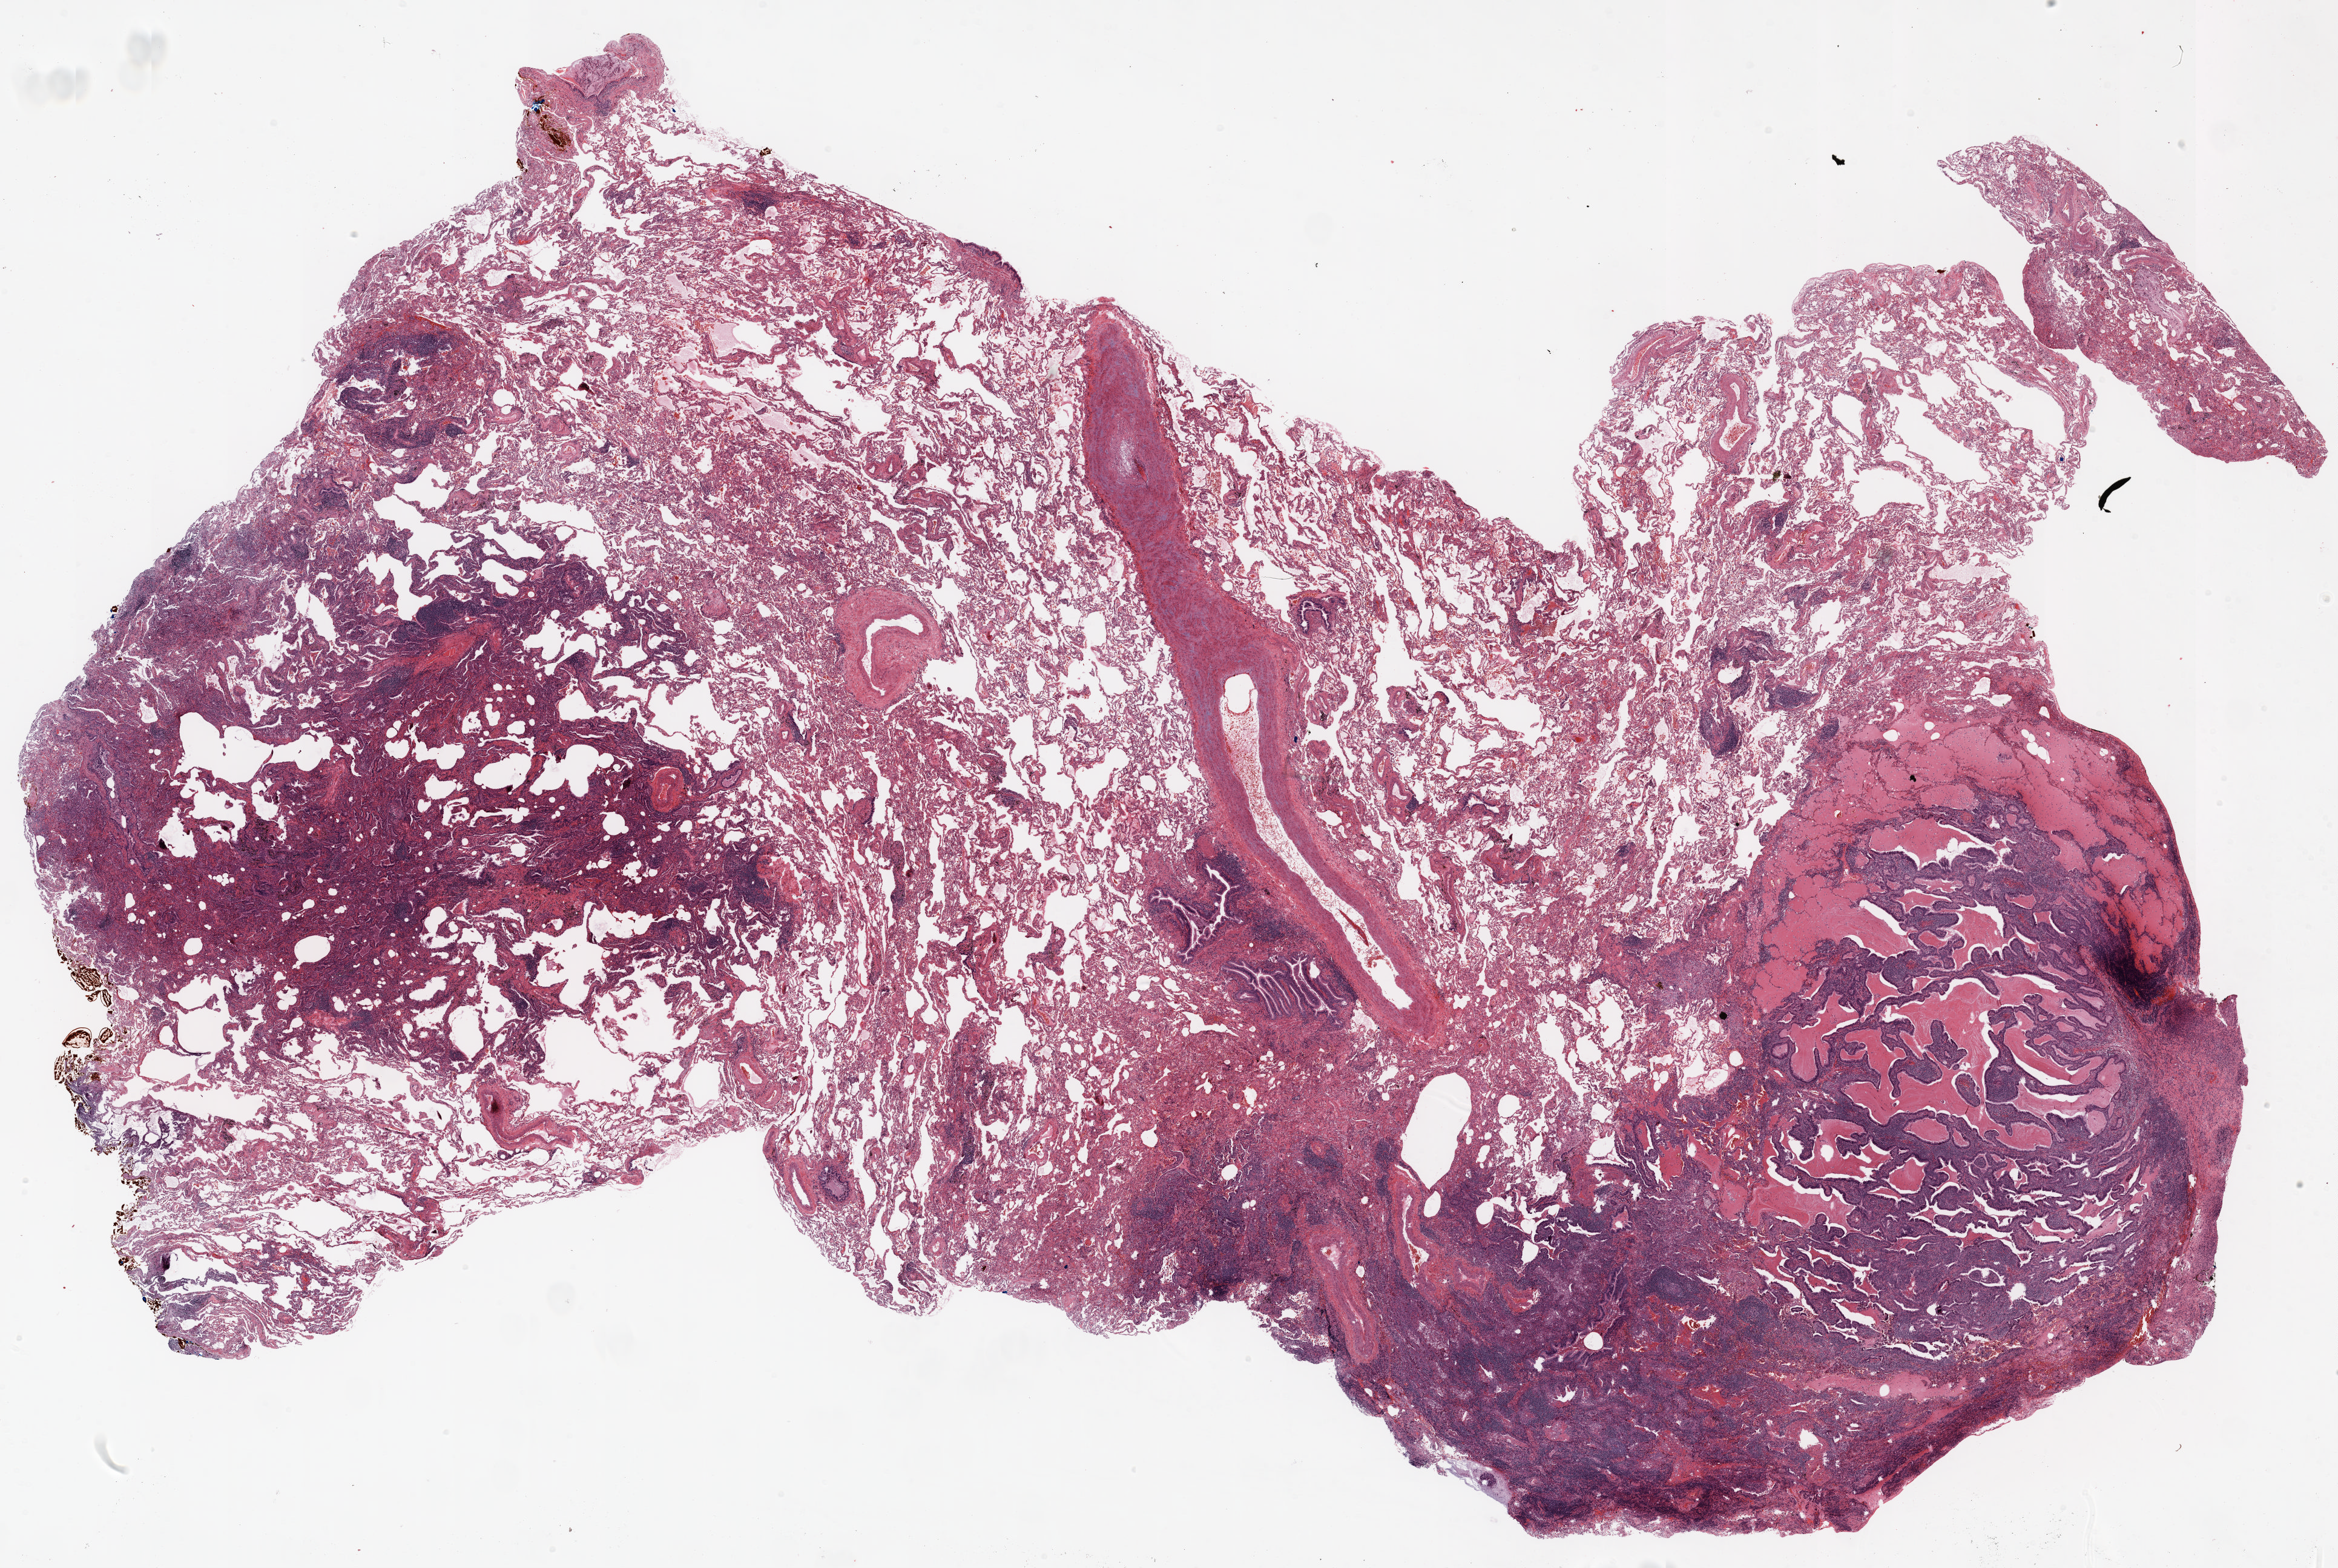
H&E whole-slide image — shown as a low-resolution overview of the whole scanned area (about 31.0 x 20.8 mm). FFPE section. Lung tissue. Female, age 72 at enrolment. Former smoker at enrolment. Grade: moderately differentiated (G2).
Participant's lung-cancer diagnosis: Adenocarcinoma, NOS (ICD-O-3 8140/3). ICD-O-3 topography: upper lobe of lung (C34.1). Tumour size (pathology): 25 mm. Stage (AJCC 6th edition): IA. Primary tumour location (clinical record): left upper lobe. Note: participant had 2 primary lung cancers recorded; fields above describe the first.